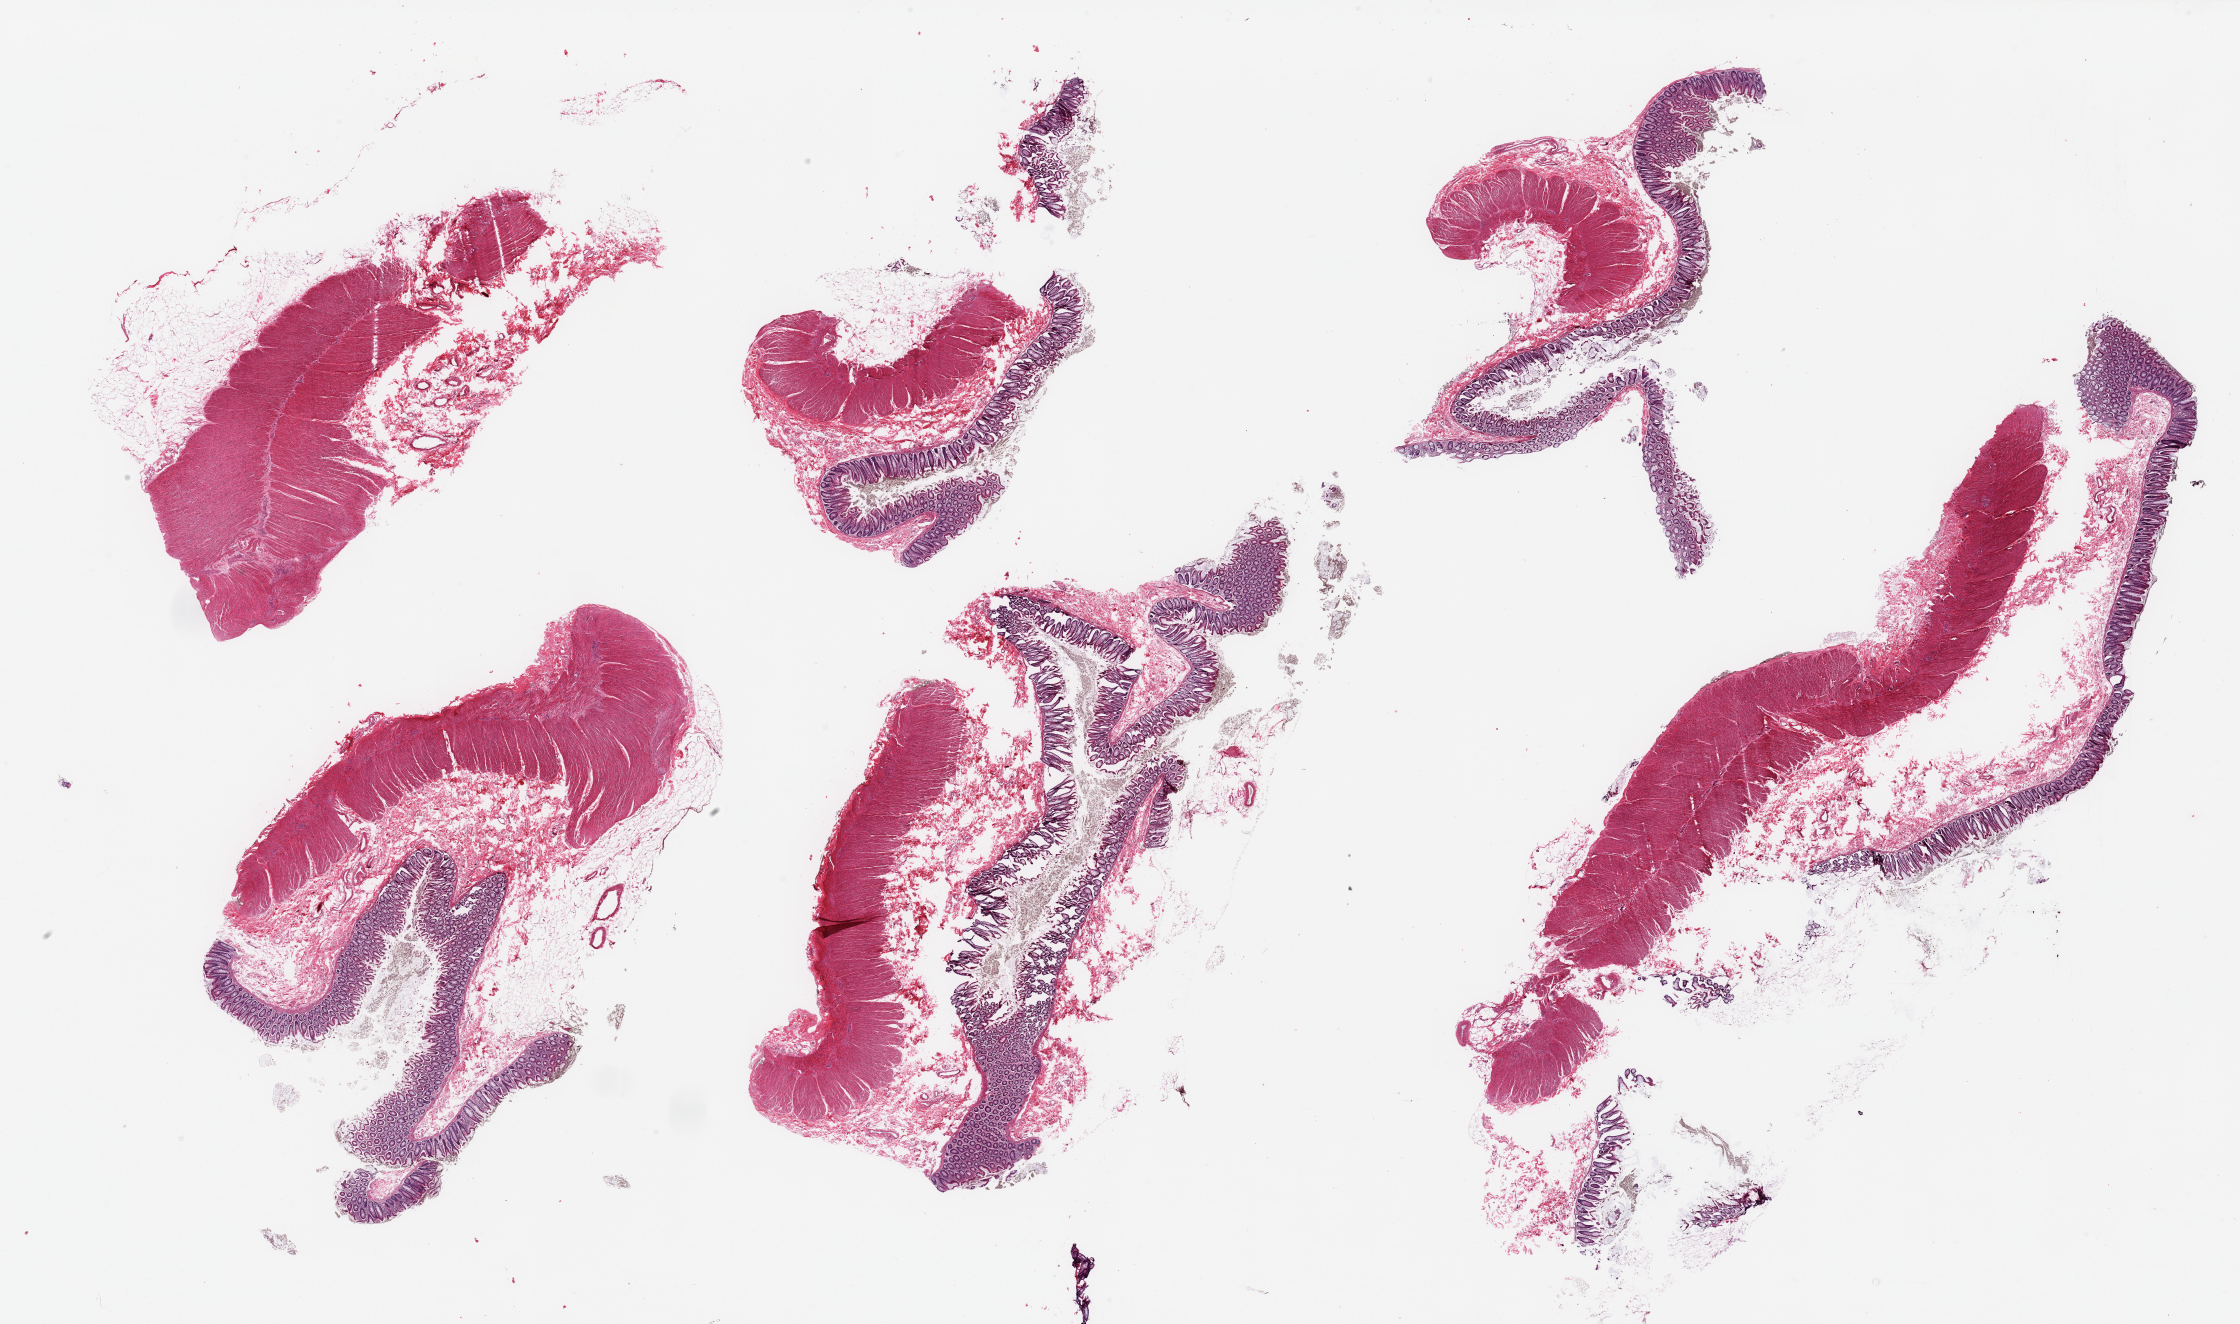
Whole-slide image, hematoxylin and eosin (H&E) stain — whole scanned area (about 35.4 x 20.9 mm, slide scanned at 20x) shown as a low-resolution overview. PAXgene-fixed paraffin-embedded (PFPE) section. Sampled site (target tissue): transverse colon. Donor tissue sample. Donor sex: female.
Review note (as recorded): 6 pieces, fragmented, target mucosa up to ~0.5mm.